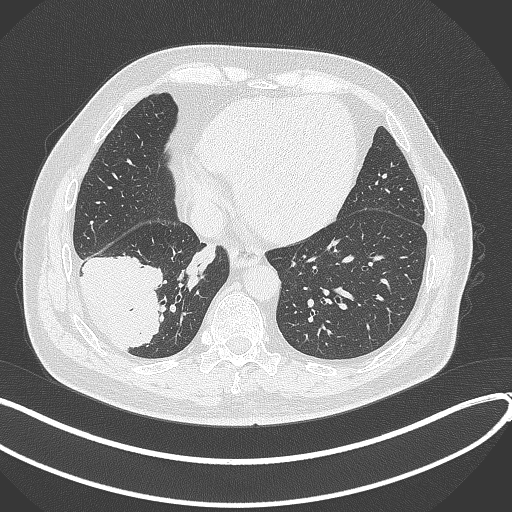
Chest CT, one axial slice; position 107 of 360 along the scan axis; lung window (W 1500 / L -600 HU); 512 × 512 image matrix, field of view 400 × 400 mm. Male patient, age 59 years.
Outlined on this slice (bounding box drawn by a radiologist):
- lung tumour (recorded histology: adenocarcinoma): bounding box (x1, y1, x2, y2) in pixels: (81, 249, 165, 353)